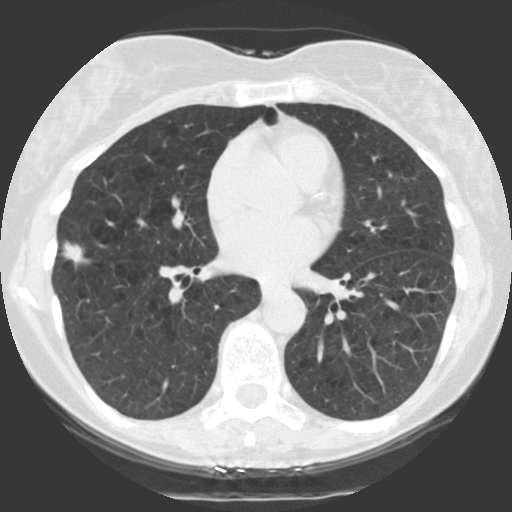
Chest CT (low-dose screening protocol), one axial image. First (baseline) screen. Lung window (W 1500 / L -600 HU). Female, age 68 years at enrolment. Former smoker at enrolment.
• Expert reader's lesion annotation, bounding box (x1, y1, x2, y2) in pixels: (50, 234, 100, 284).
• The screening reader recorded 2 non-calcified nodules or masses ≥4 mm on this exam (right lower lobe, right middle lobe); which of them this box marks is not recorded.
• Lung cancer was diagnosed 40 days after this screen: bronchiolo-alveolar adenocarcinoma, NOS, right upper lobe, right middle lobe, right lower lobe, well differentiated (G1), stage IV (AJCC 6th edition).